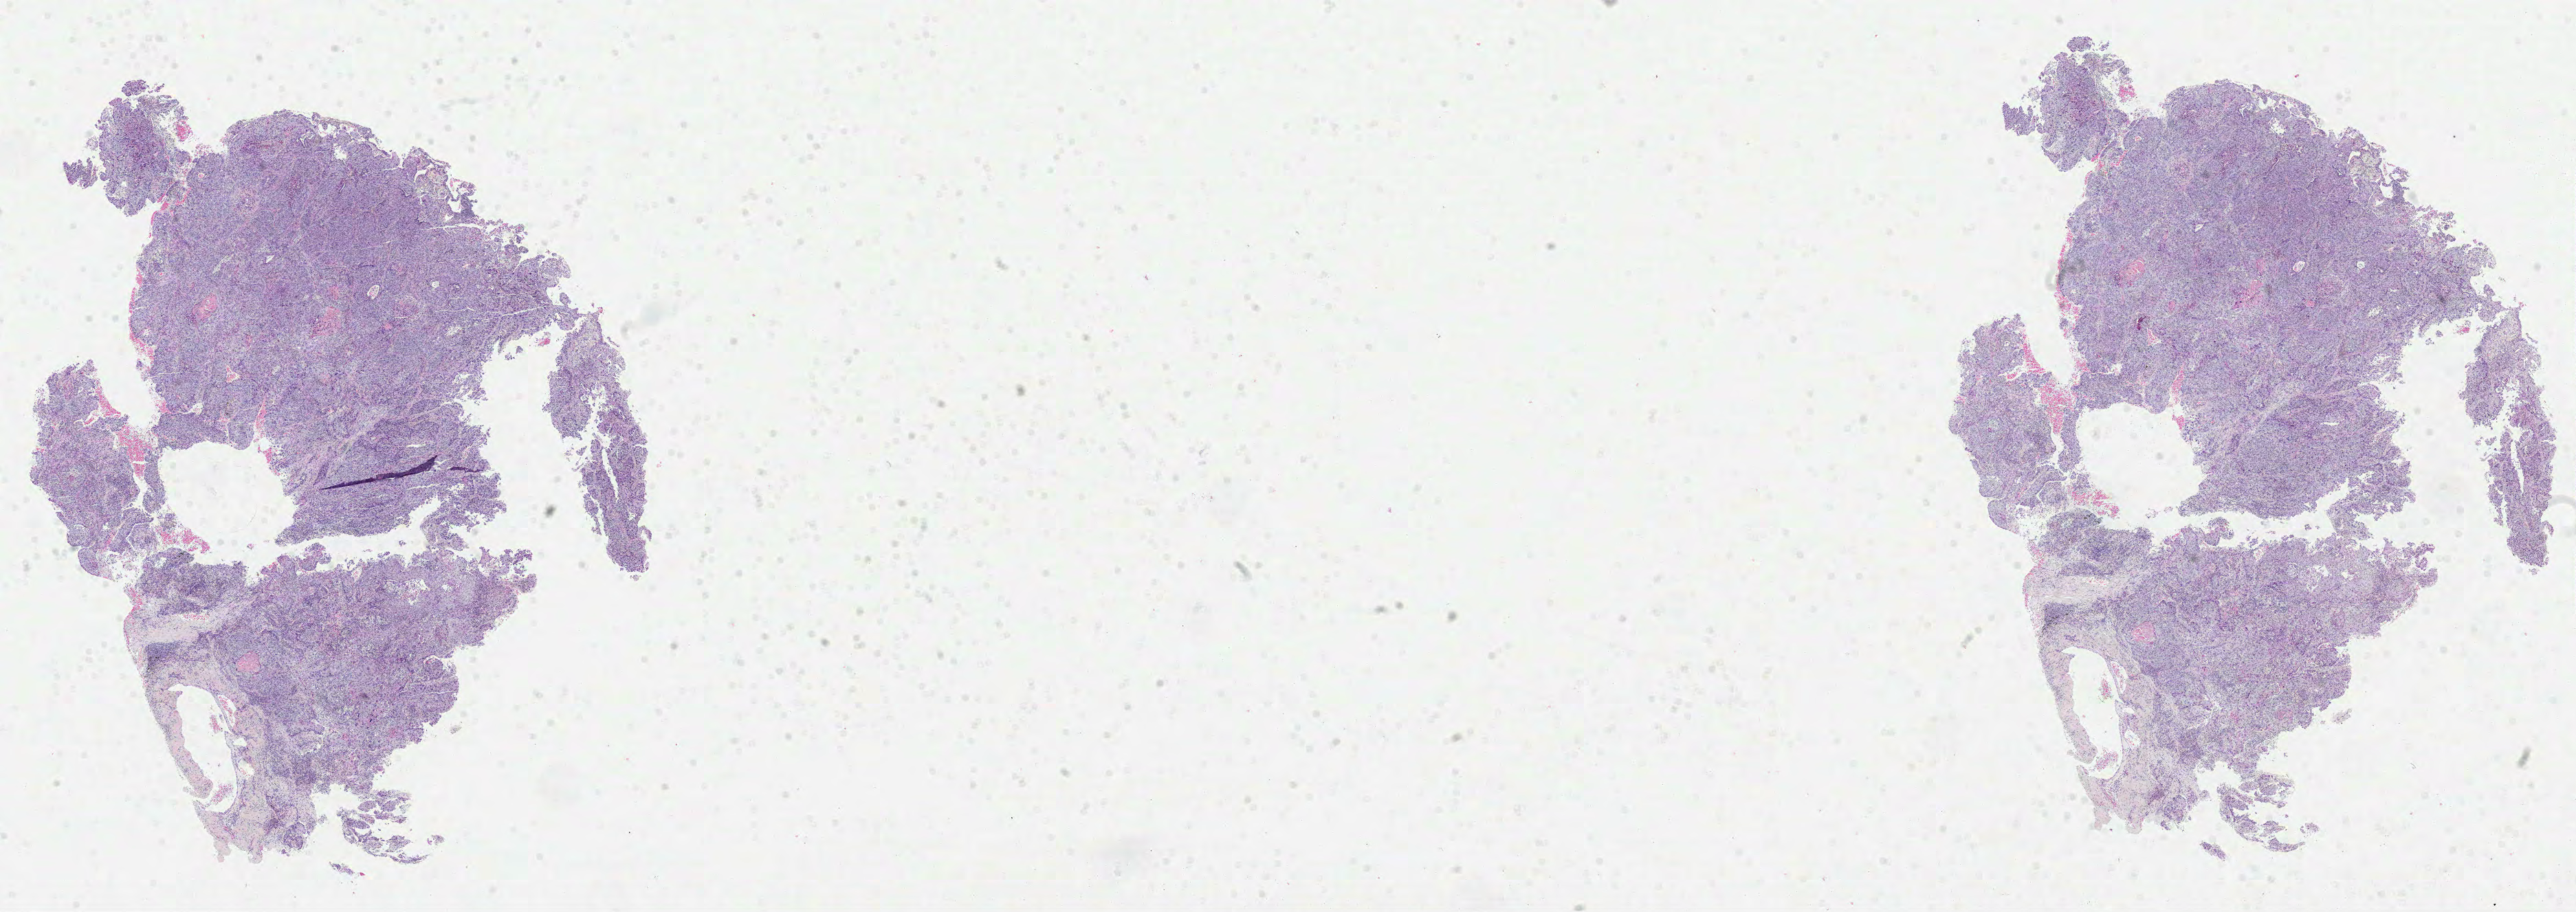
Digitized H&E-stained tissue section (whole slide) — a low-resolution overview of the entire scanned area, about 30.2 x 10.7 mm. FFPE section. Sample: primary tumour, lung. Patient: male, age at initial diagnosis 71 years.
AJCC pathologic stage: IB (6th edition). Pathologic diagnosis: Squamous cell carcinoma, NOS (middle lobe, lung).